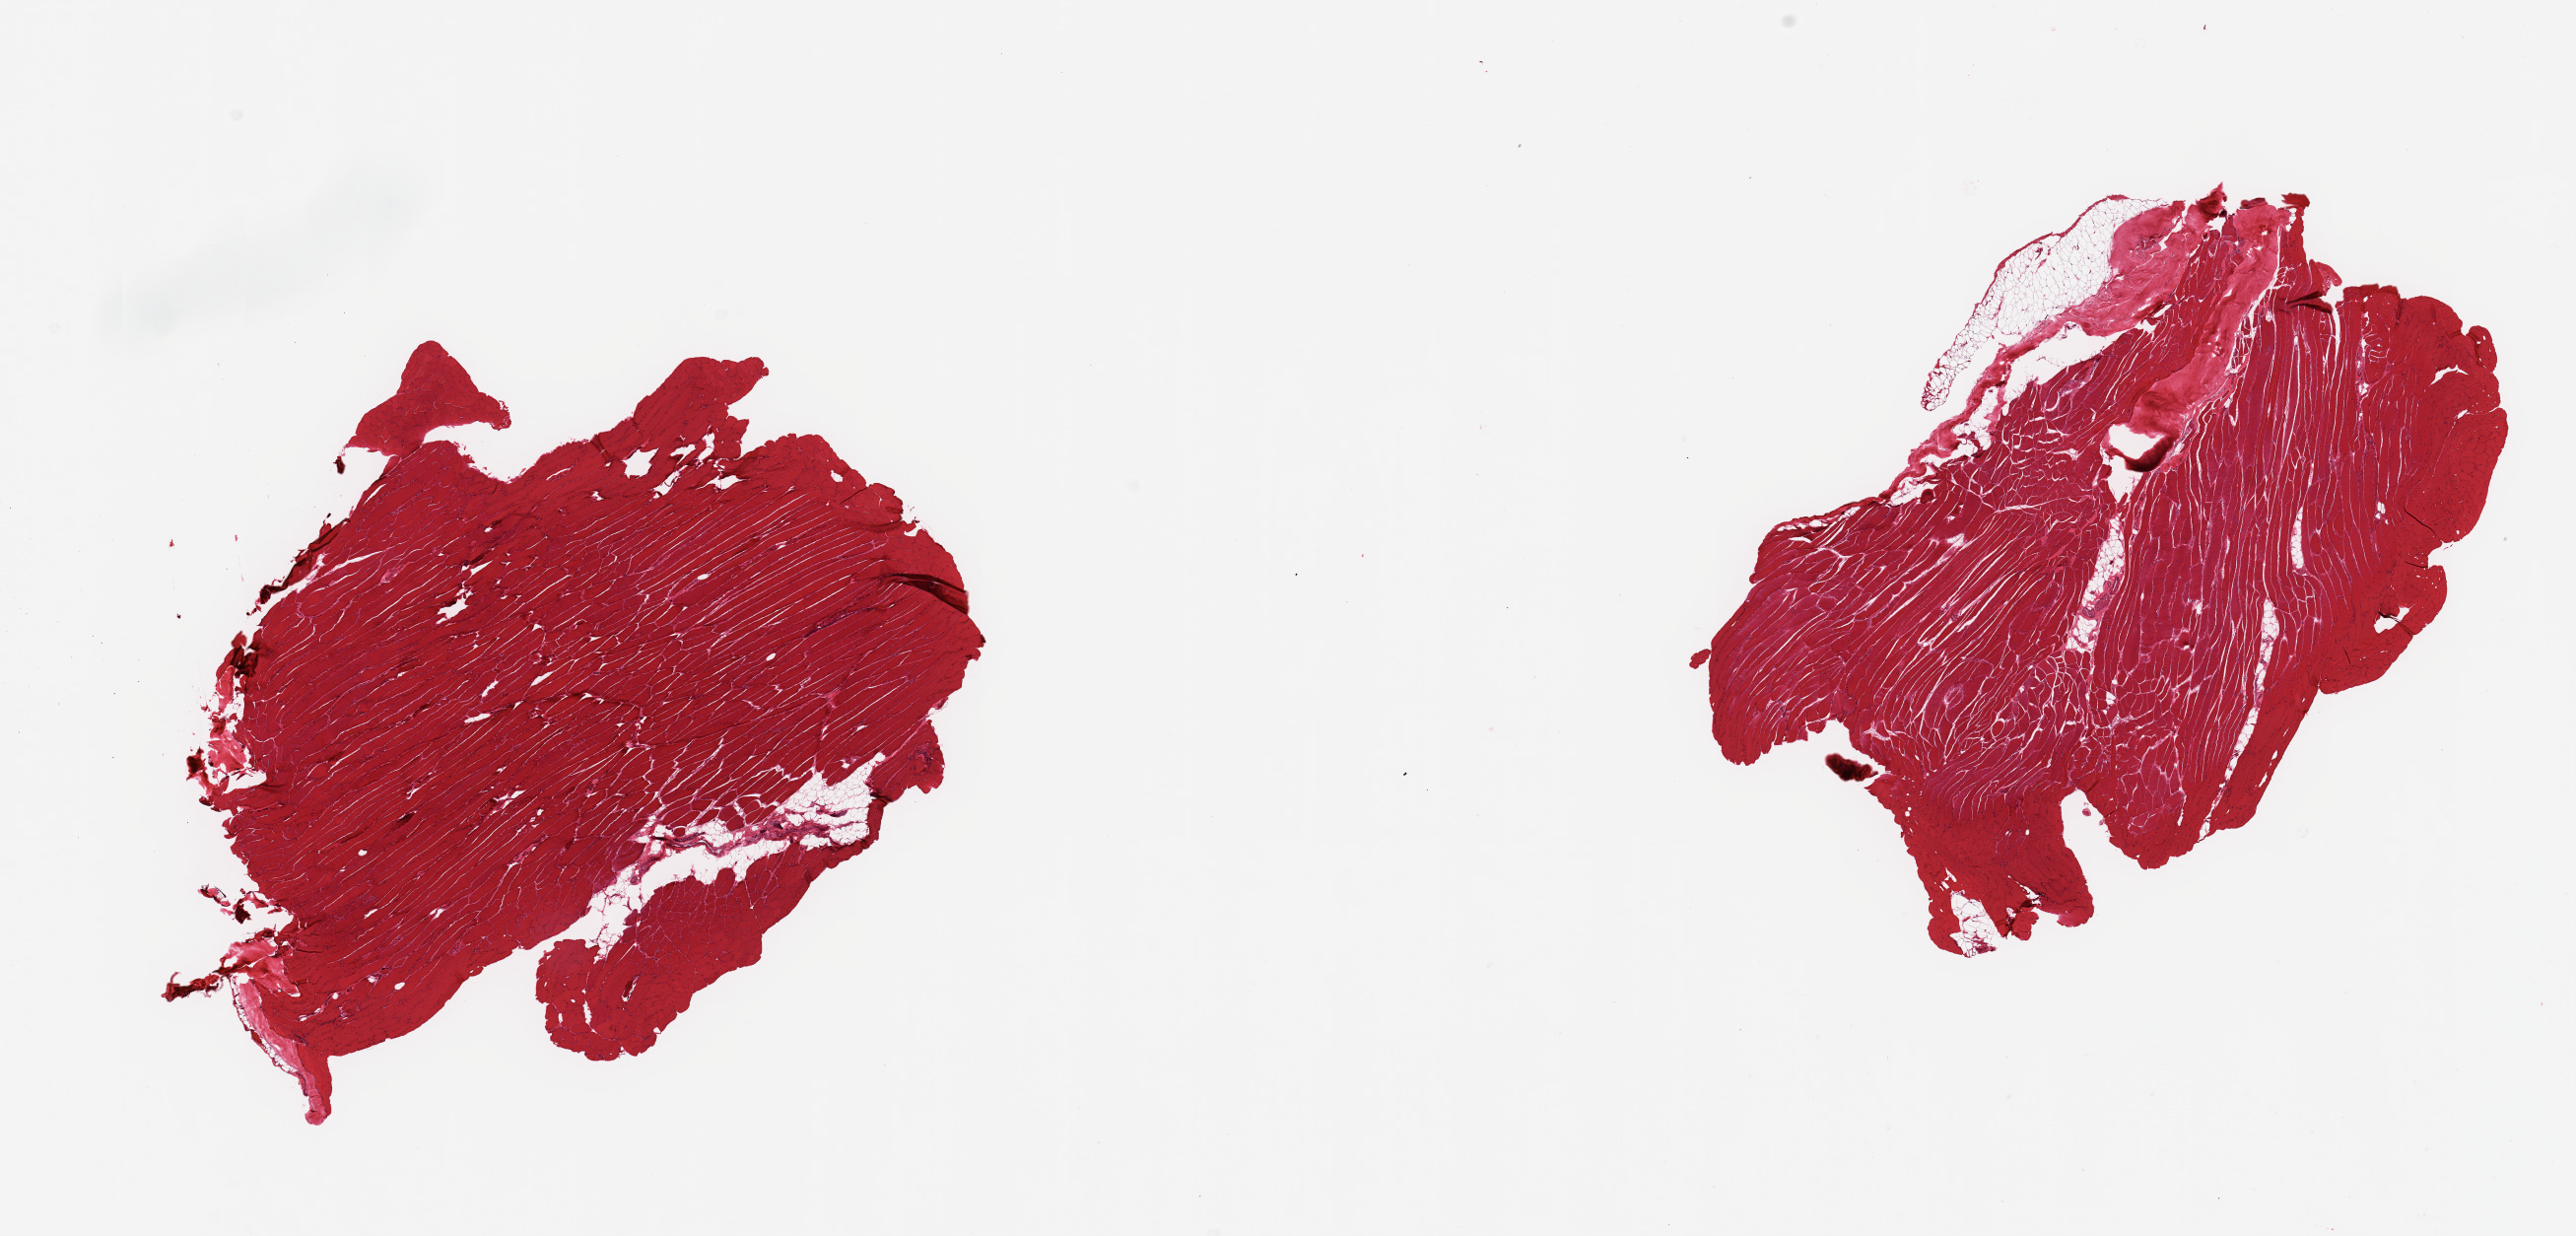
Whole-slide image, hematoxylin and eosin (H&E) stain, a low-resolution overview of the entire scanned area, about 20.7 x 9.9 mm; PAXgene-fixed, paraffin-embedded tissue; sampled site (target tissue): skeletal muscle; donor tissue sample. Donor sex: male.
Review note (as recorded): 2 pieces; one contains 10% internal fat and other 5% internal and 5% external fat.